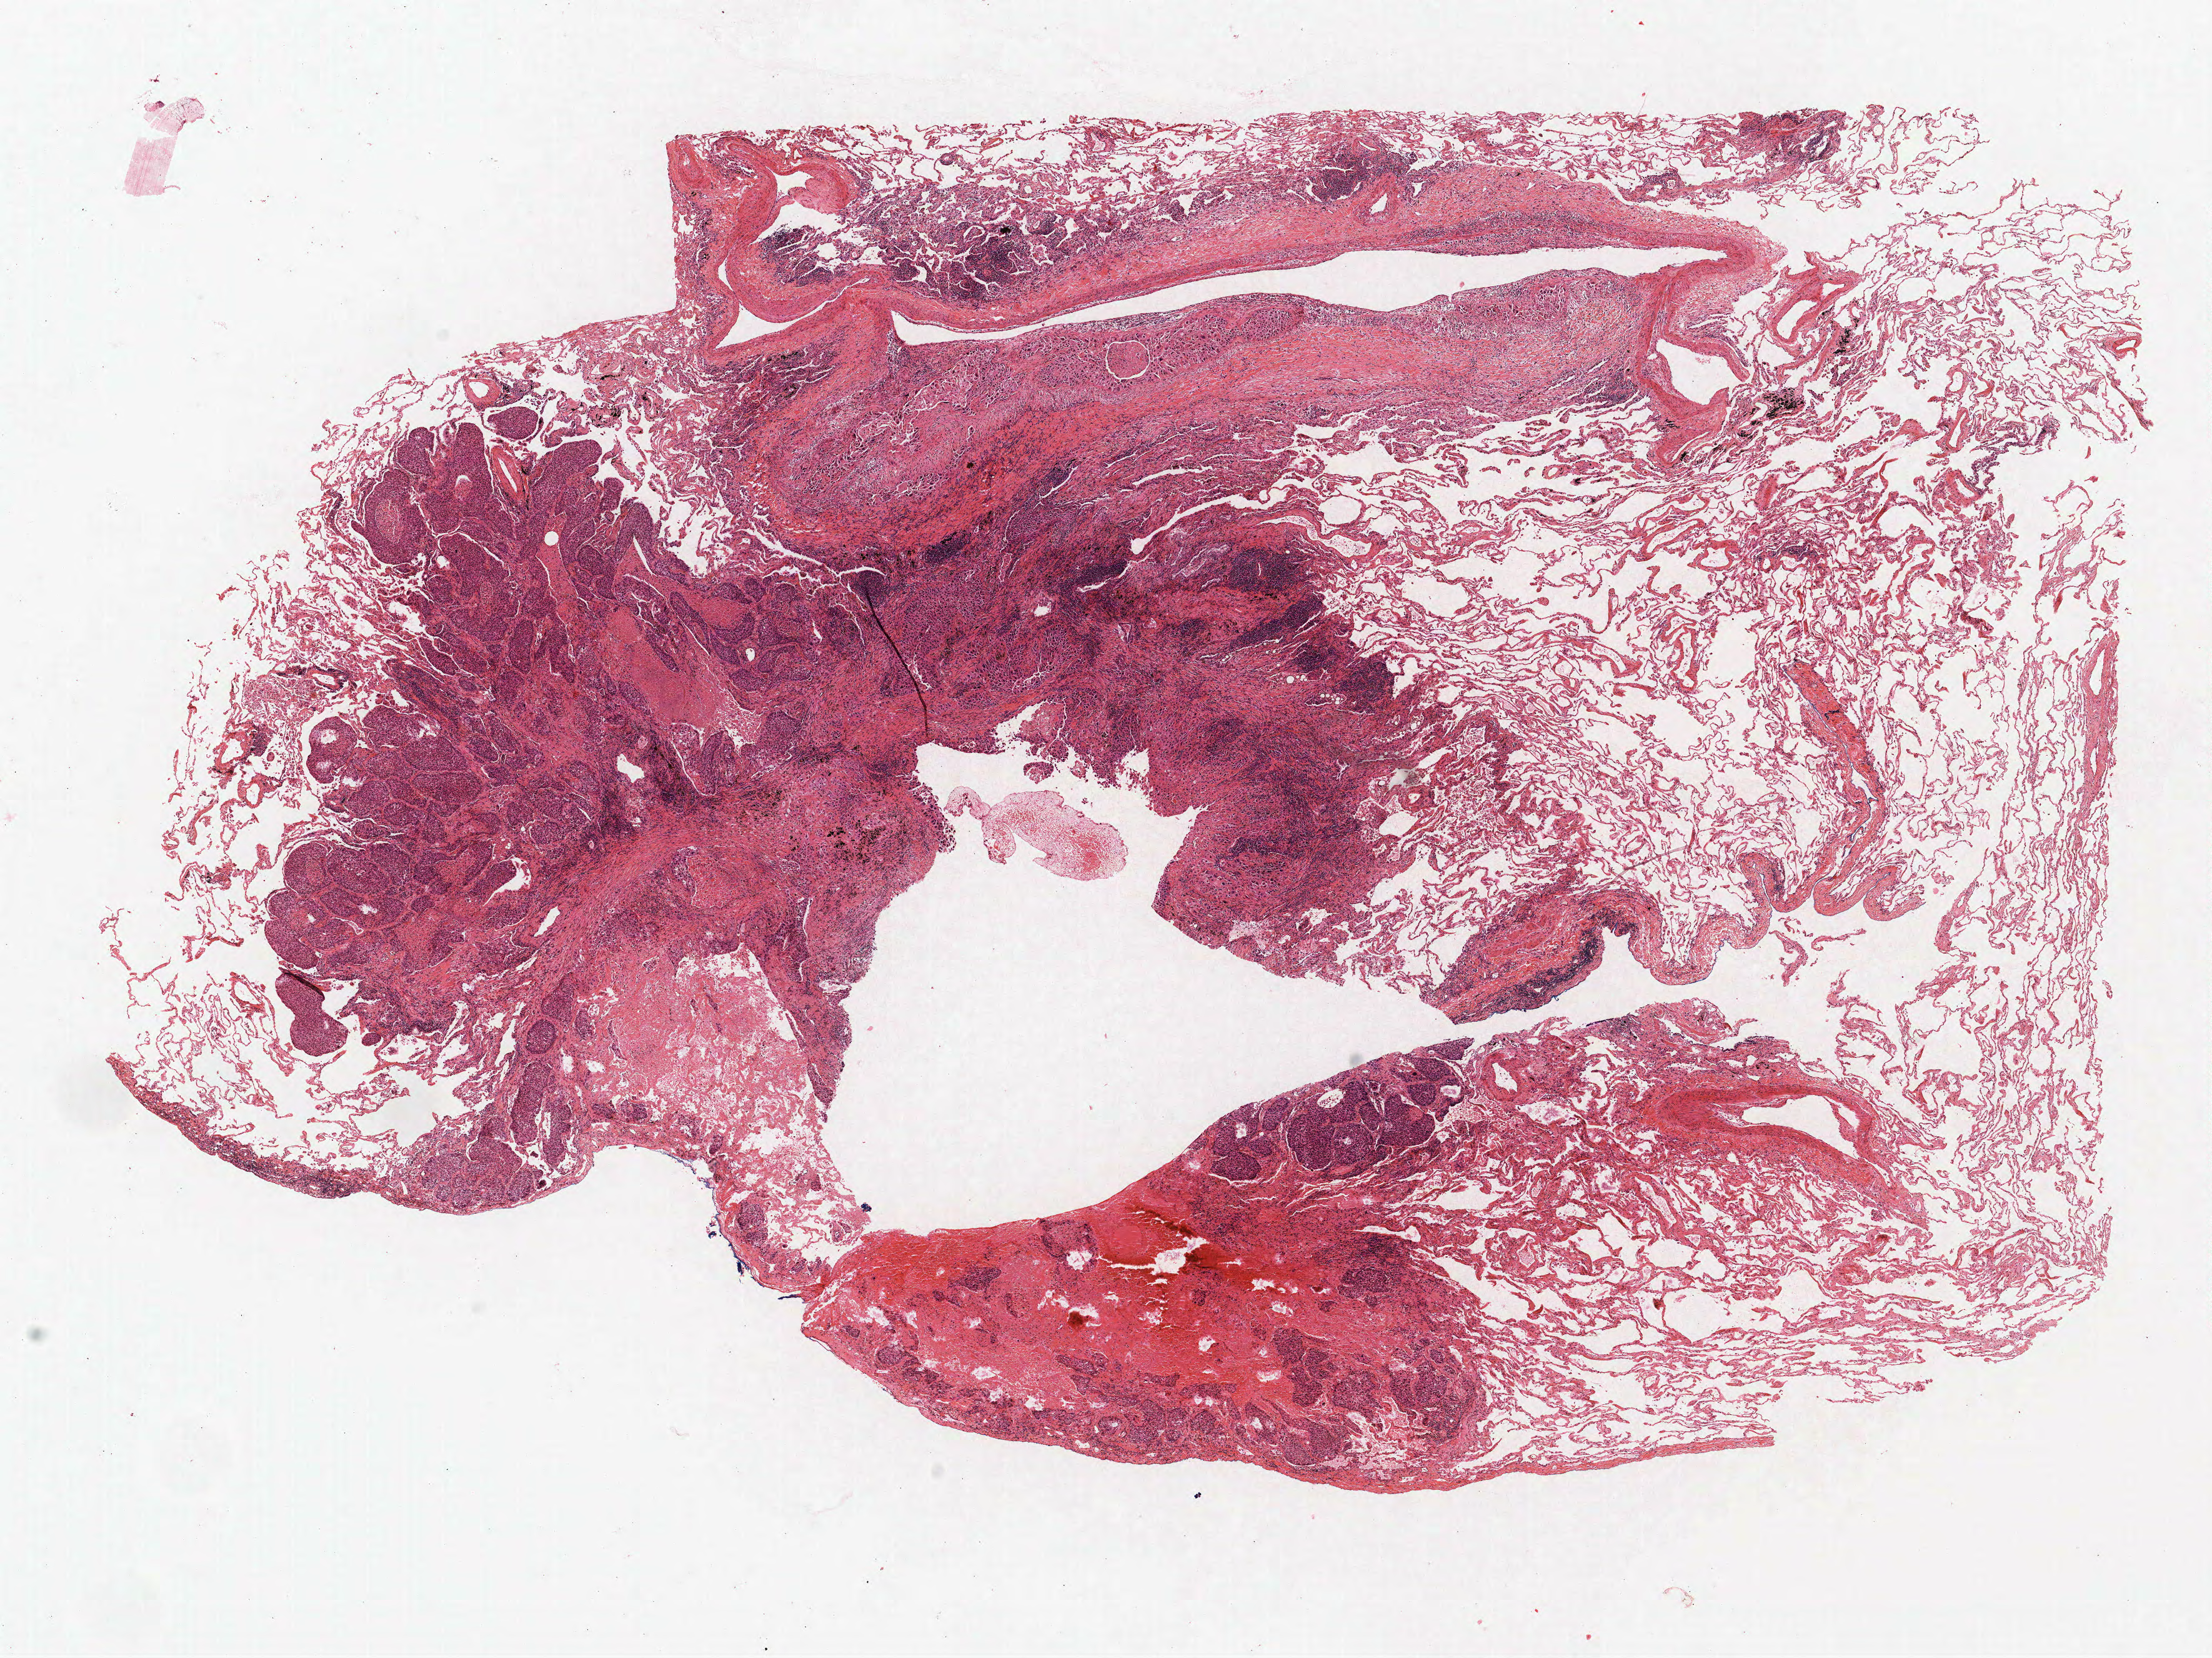
Whole-slide histology image, Hematoxylin and eosin (H&E) stained, shown as a low-resolution overview of the whole scanned area (about 14.2 x 10.6 mm, from a 40x scan), FFPE section, lung tissue. Female patient, aged 63 at enrolment. Grade: moderately differentiated (G2).
• primary tumour location (clinical record): left lower lobe
• tumour size (pathology): 15 mm
• stage (AJCC 6th edition): IB
• participant's lung-cancer diagnosis: Squamous cell carcinoma, NOS (ICD-O-3 8070/3)